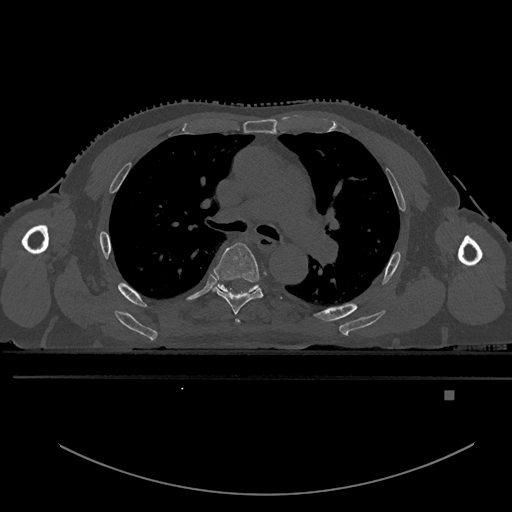
CT including the spine, one axial slice. Position 351 of 969 along the scan axis. Bone window (W 1800 / L 400 HU). 0.5 mm slice thickness. 512 × 512 image matrix, field of view 456 × 456 mm. Patient: male, 82 years. Case-level facts recorded for this patient, not image findings: primary cancer: prostate; vertebrae with lytic lesions (as recorded): T11, T9, T8, T2.
Structures marked on this image (semi-automatic segmentation, software-assisted and operator-edited):
- T4 vertebra: bounding box <235,319,240,323> (left, top, right, bottom; pixels)
- T5 vertebra: <213,242,263,315>
- T6 vertebra: <212,283,259,294>